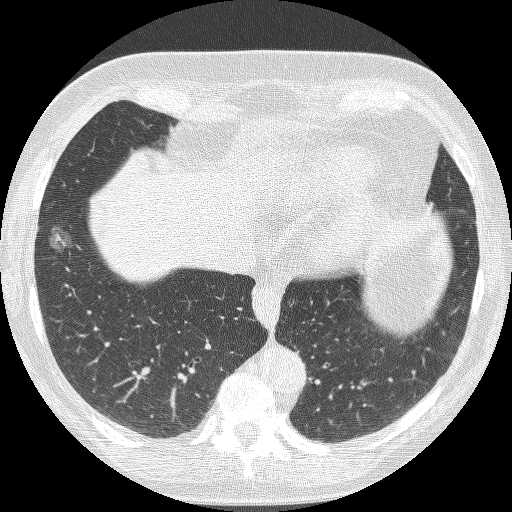
Chest CT (low-dose screening protocol), one axial image. Baseline annual screen. Lung window (W 1500 / L -600 HU). 1.25 mm slice thickness. Lung (sharp) reconstruction kernel (BONE). Slice 67 of 221 in the series. Female, age 68 years at enrolment. Current smoker at enrolment.
- Expert-annotated lung lesion, box from (x=34, y=219) to (x=86, y=268) px.
- Reader record for this screening exam (exam-level; its link to the box is not recorded): non-calcified nodule or mass ≥4 mm, right lower lobe, 16 × 12 mm, poorly defined margins, ground glass attenuation.
- Lung cancer was diagnosed 406 days after this screen (after the second annual screen): bronchiolo-alveolar adenocarcinoma, NOS, right lower lobe, well differentiated (G1), stage IA (AJCC 6th edition), 13 mm at pathology.